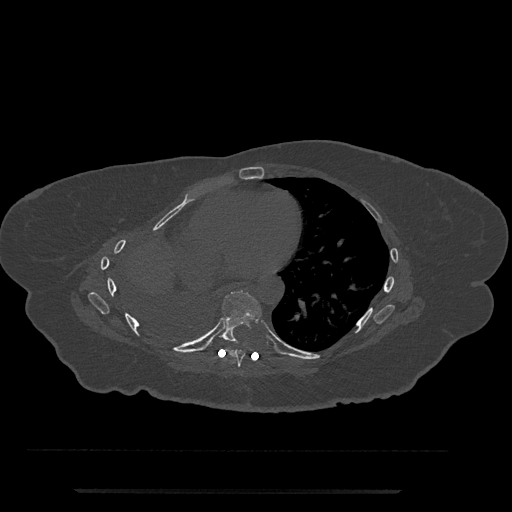
CT including the spine, one axial slice; position 413 of 797 along the scan axis; reconstruction kernel Br40s/3; bone window (W 1800 / L 400 HU); 0.5 mm slice thickness; 512 × 512 image matrix, field of view 440 × 440 mm. Patient: female, 51 years. From the clinical record (not read from this slice): primary cancer: neuro.
Annotated regions visible in this slice (semi-automatic segmentation, software-assisted and operator-edited):
- T7 vertebra: box from (x=224, y=348) to (x=245, y=367) px
- T8 vertebra: (x=219, y=290)–(x=262, y=342)